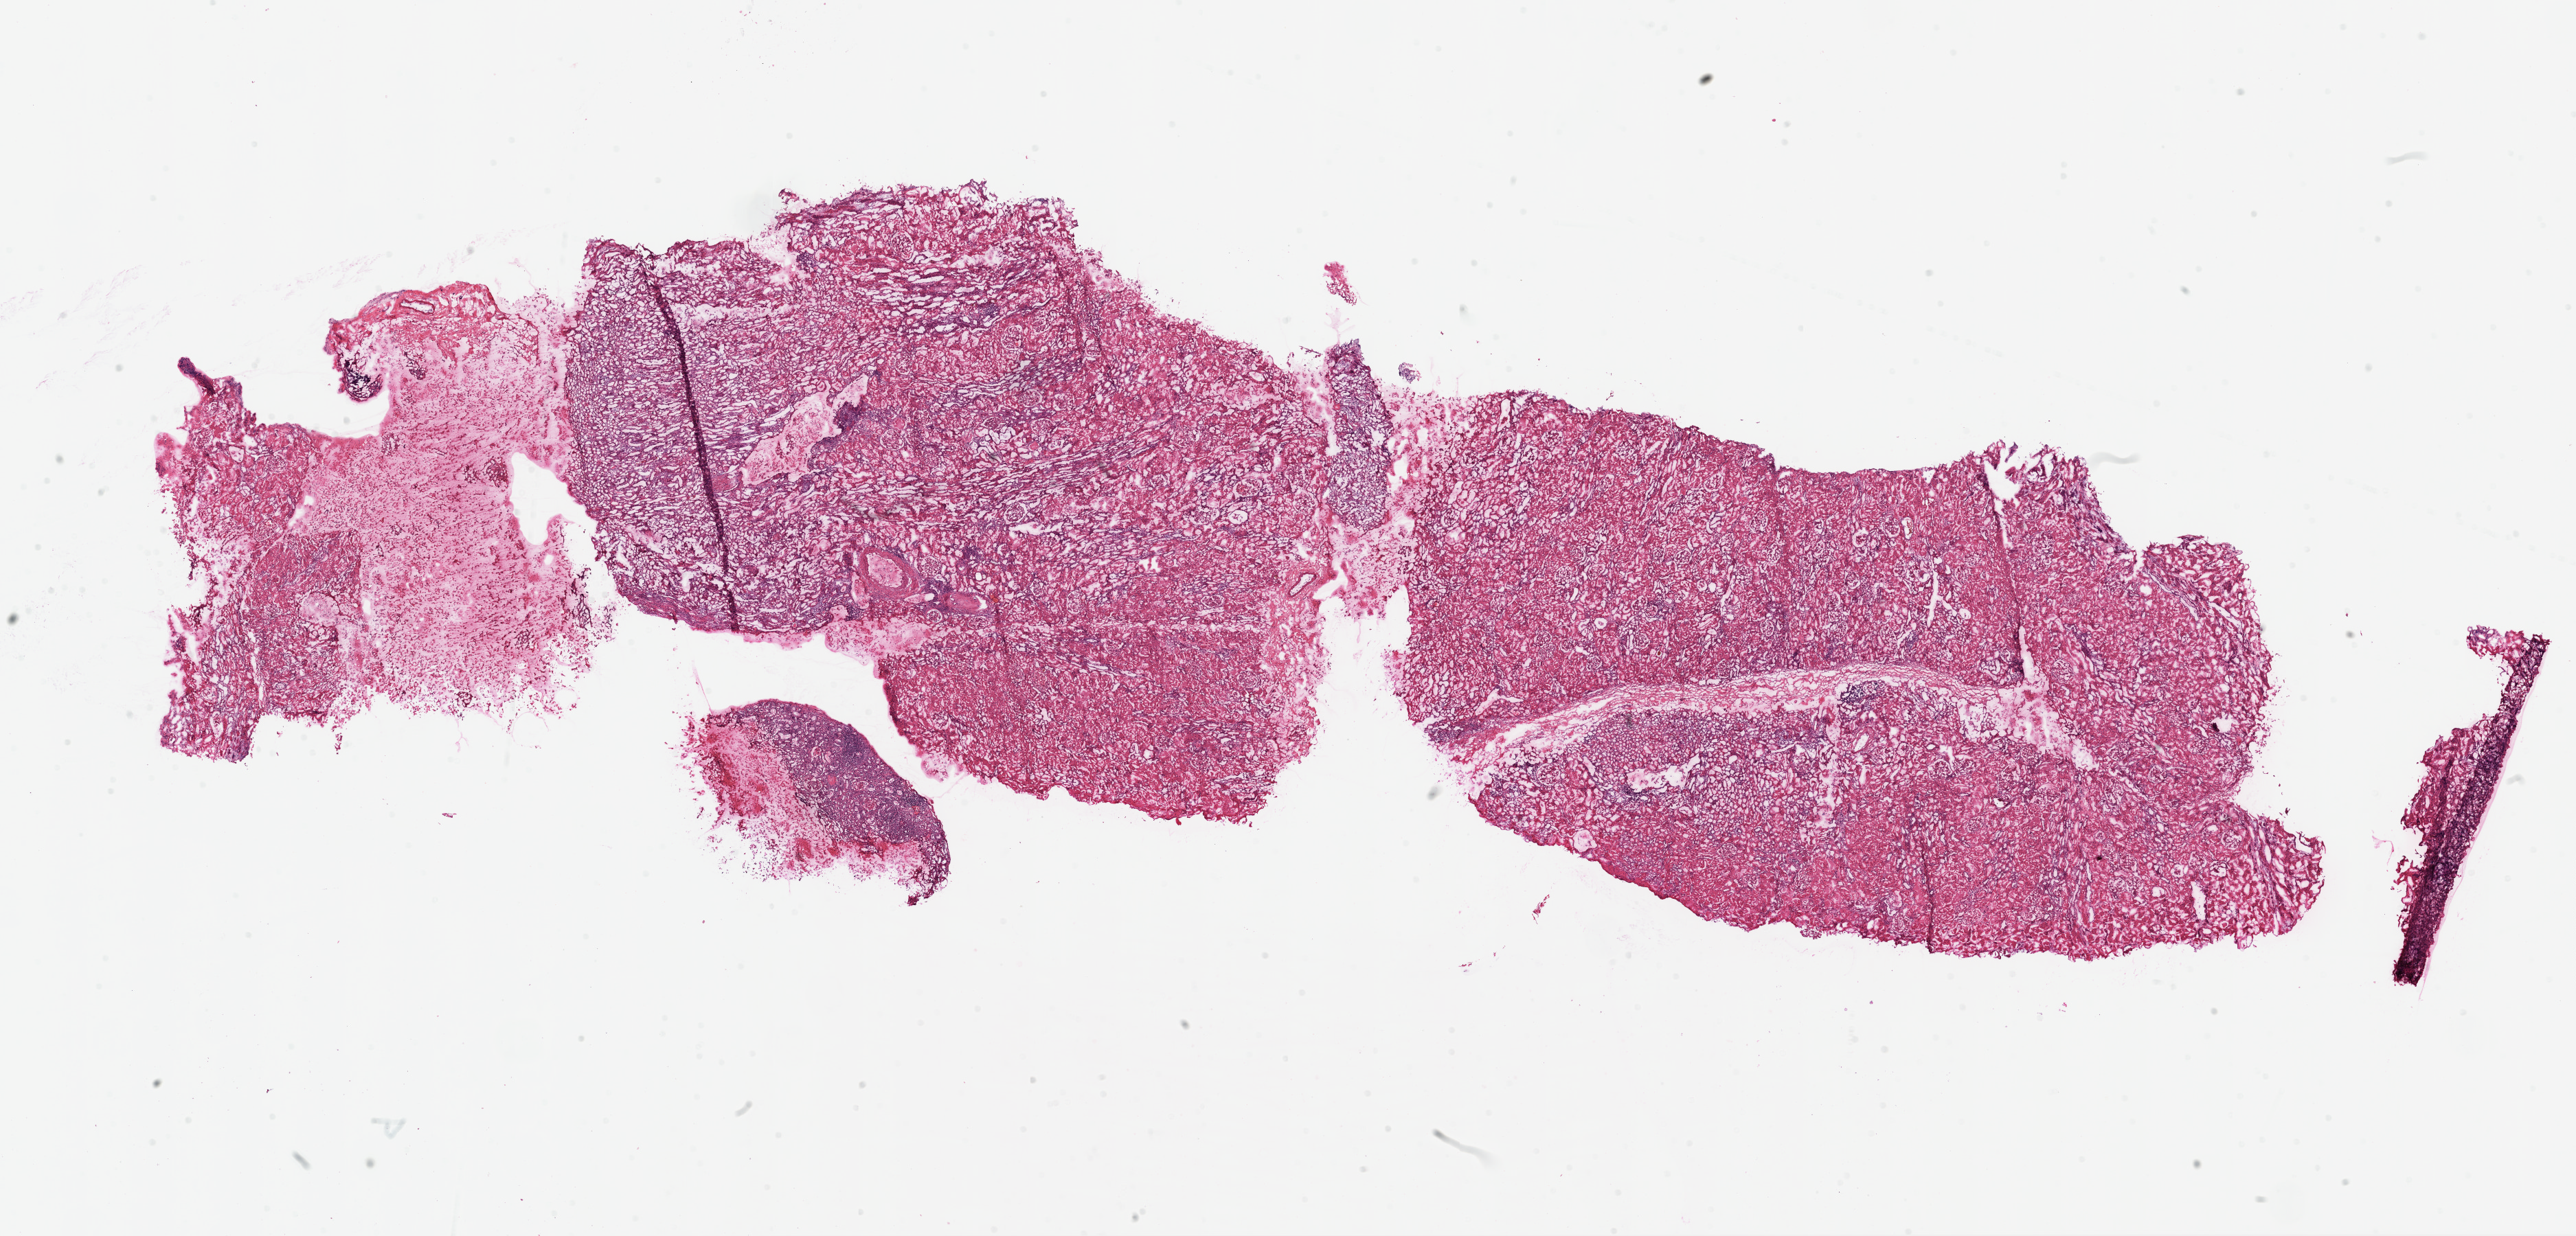
Hematoxylin and eosin (H&E) stained whole-slide image — a low-resolution overview of the entire scanned area, about 30.1 x 14.4 mm, frozen section from the top of the tissue portion, solid tissue normal (non-tumour tissue) sample from the kidney. Male, age 51 years at initial diagnosis.
* this section: solid tissue normal (non-tumour) sample from the same patient
* patient diagnosis: Clear cell adenocarcinoma, NOS